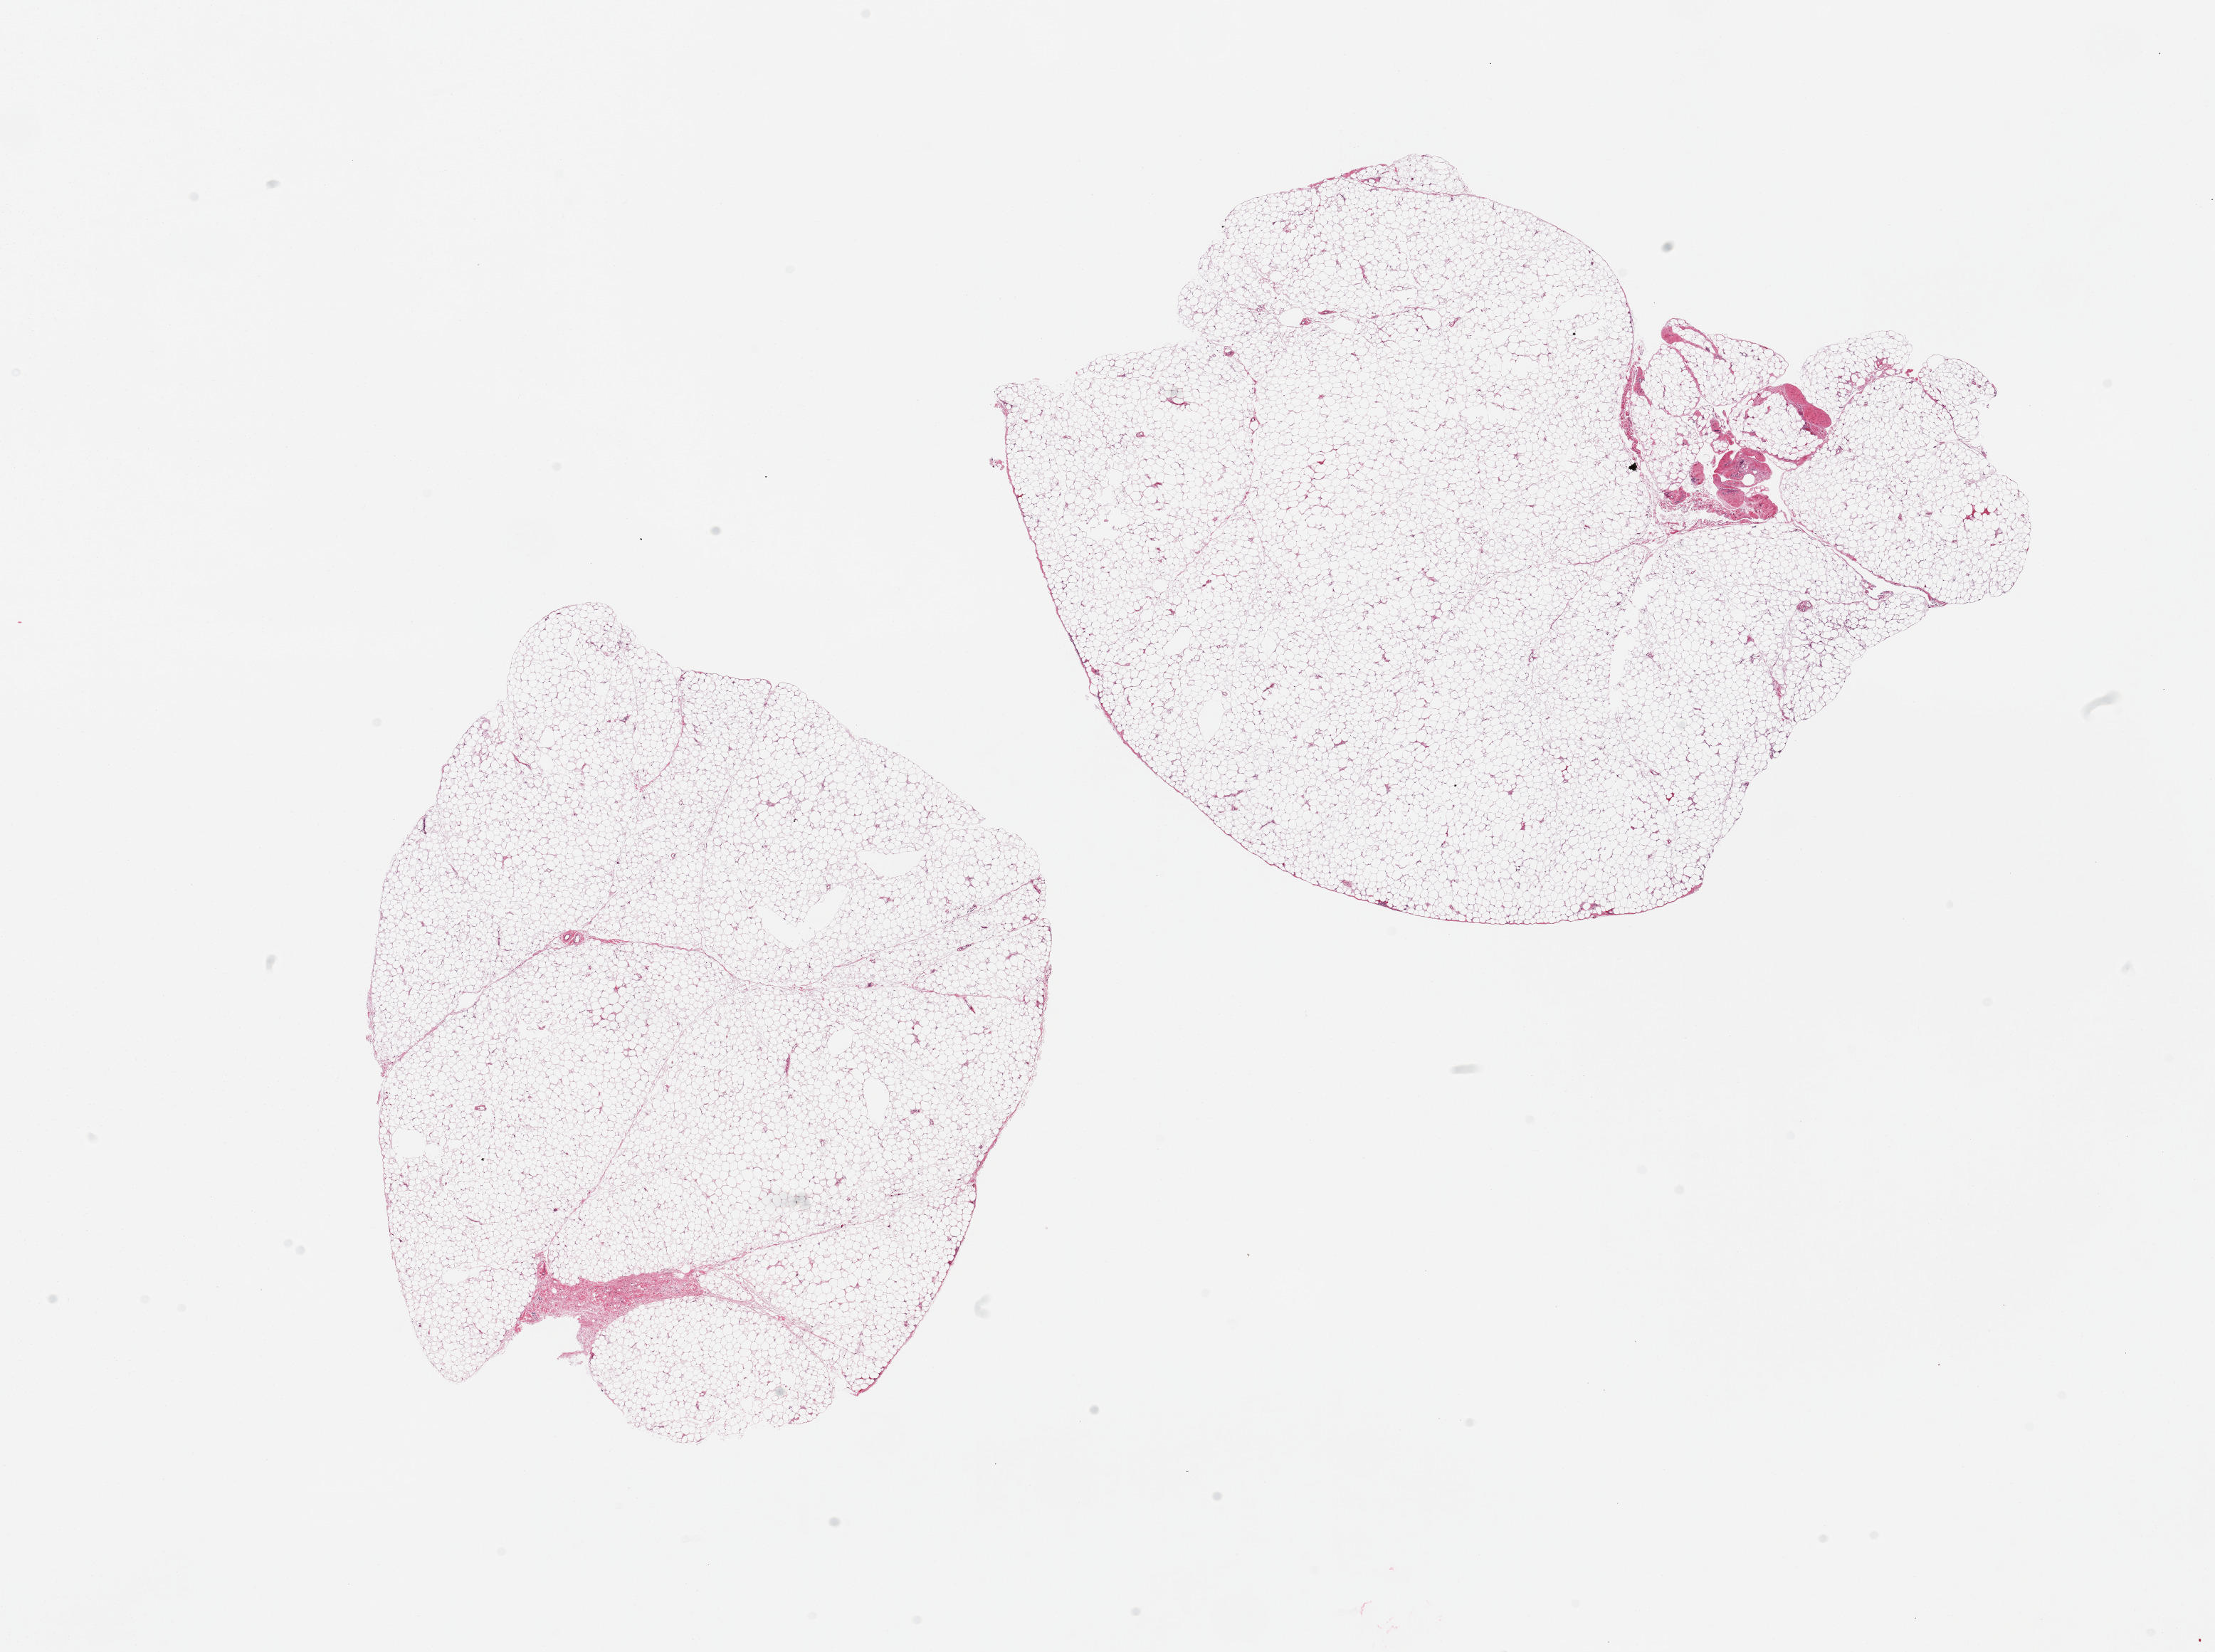
Hematoxylin and eosin (H&E) whole-slide image — a low-resolution overview of the entire scanned area, about 24.6 x 18.4 mm, PAXgene-fixed, paraffin-embedded tissue, sampled site (target tissue): omentum, donor tissue sample. Male donor.
Review note (as recorded): 2 pieces, ~5% fascia.